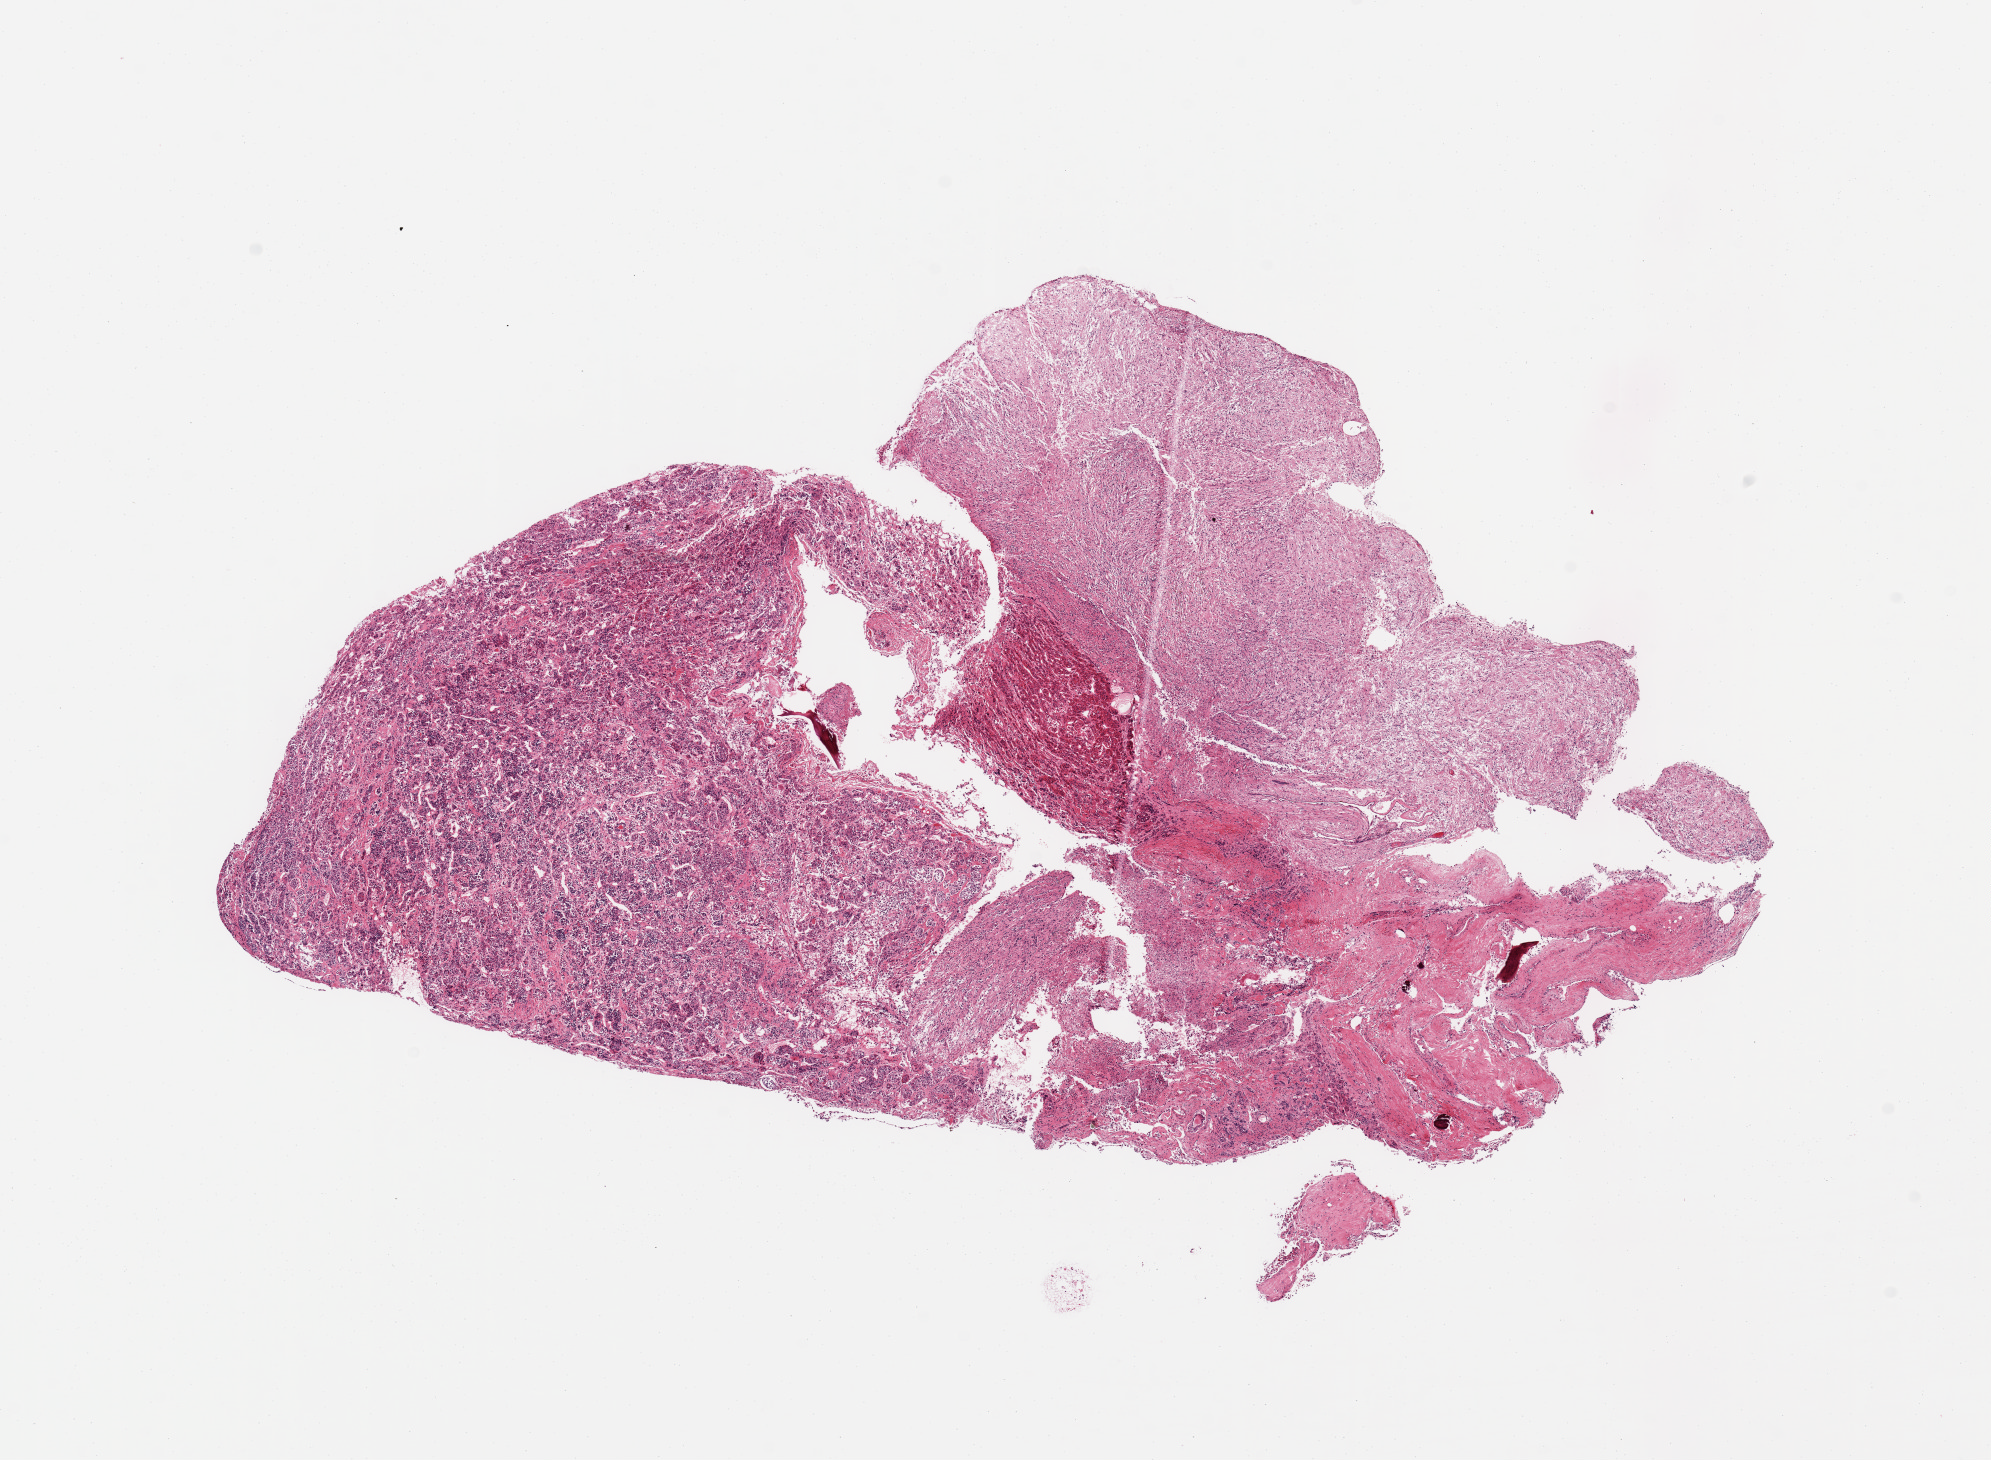
Whole-slide image, hematoxylin and eosin (H&E) stain — a low-resolution overview of the entire scanned area, about 15.8 x 11.5 mm (acquisition: 20x scan), PAXgene-fixed, paraffin-embedded tissue, sampled site (target tissue): pituitary, tissue donor sample.
Pathologist's review note for this sample: 1 piece.